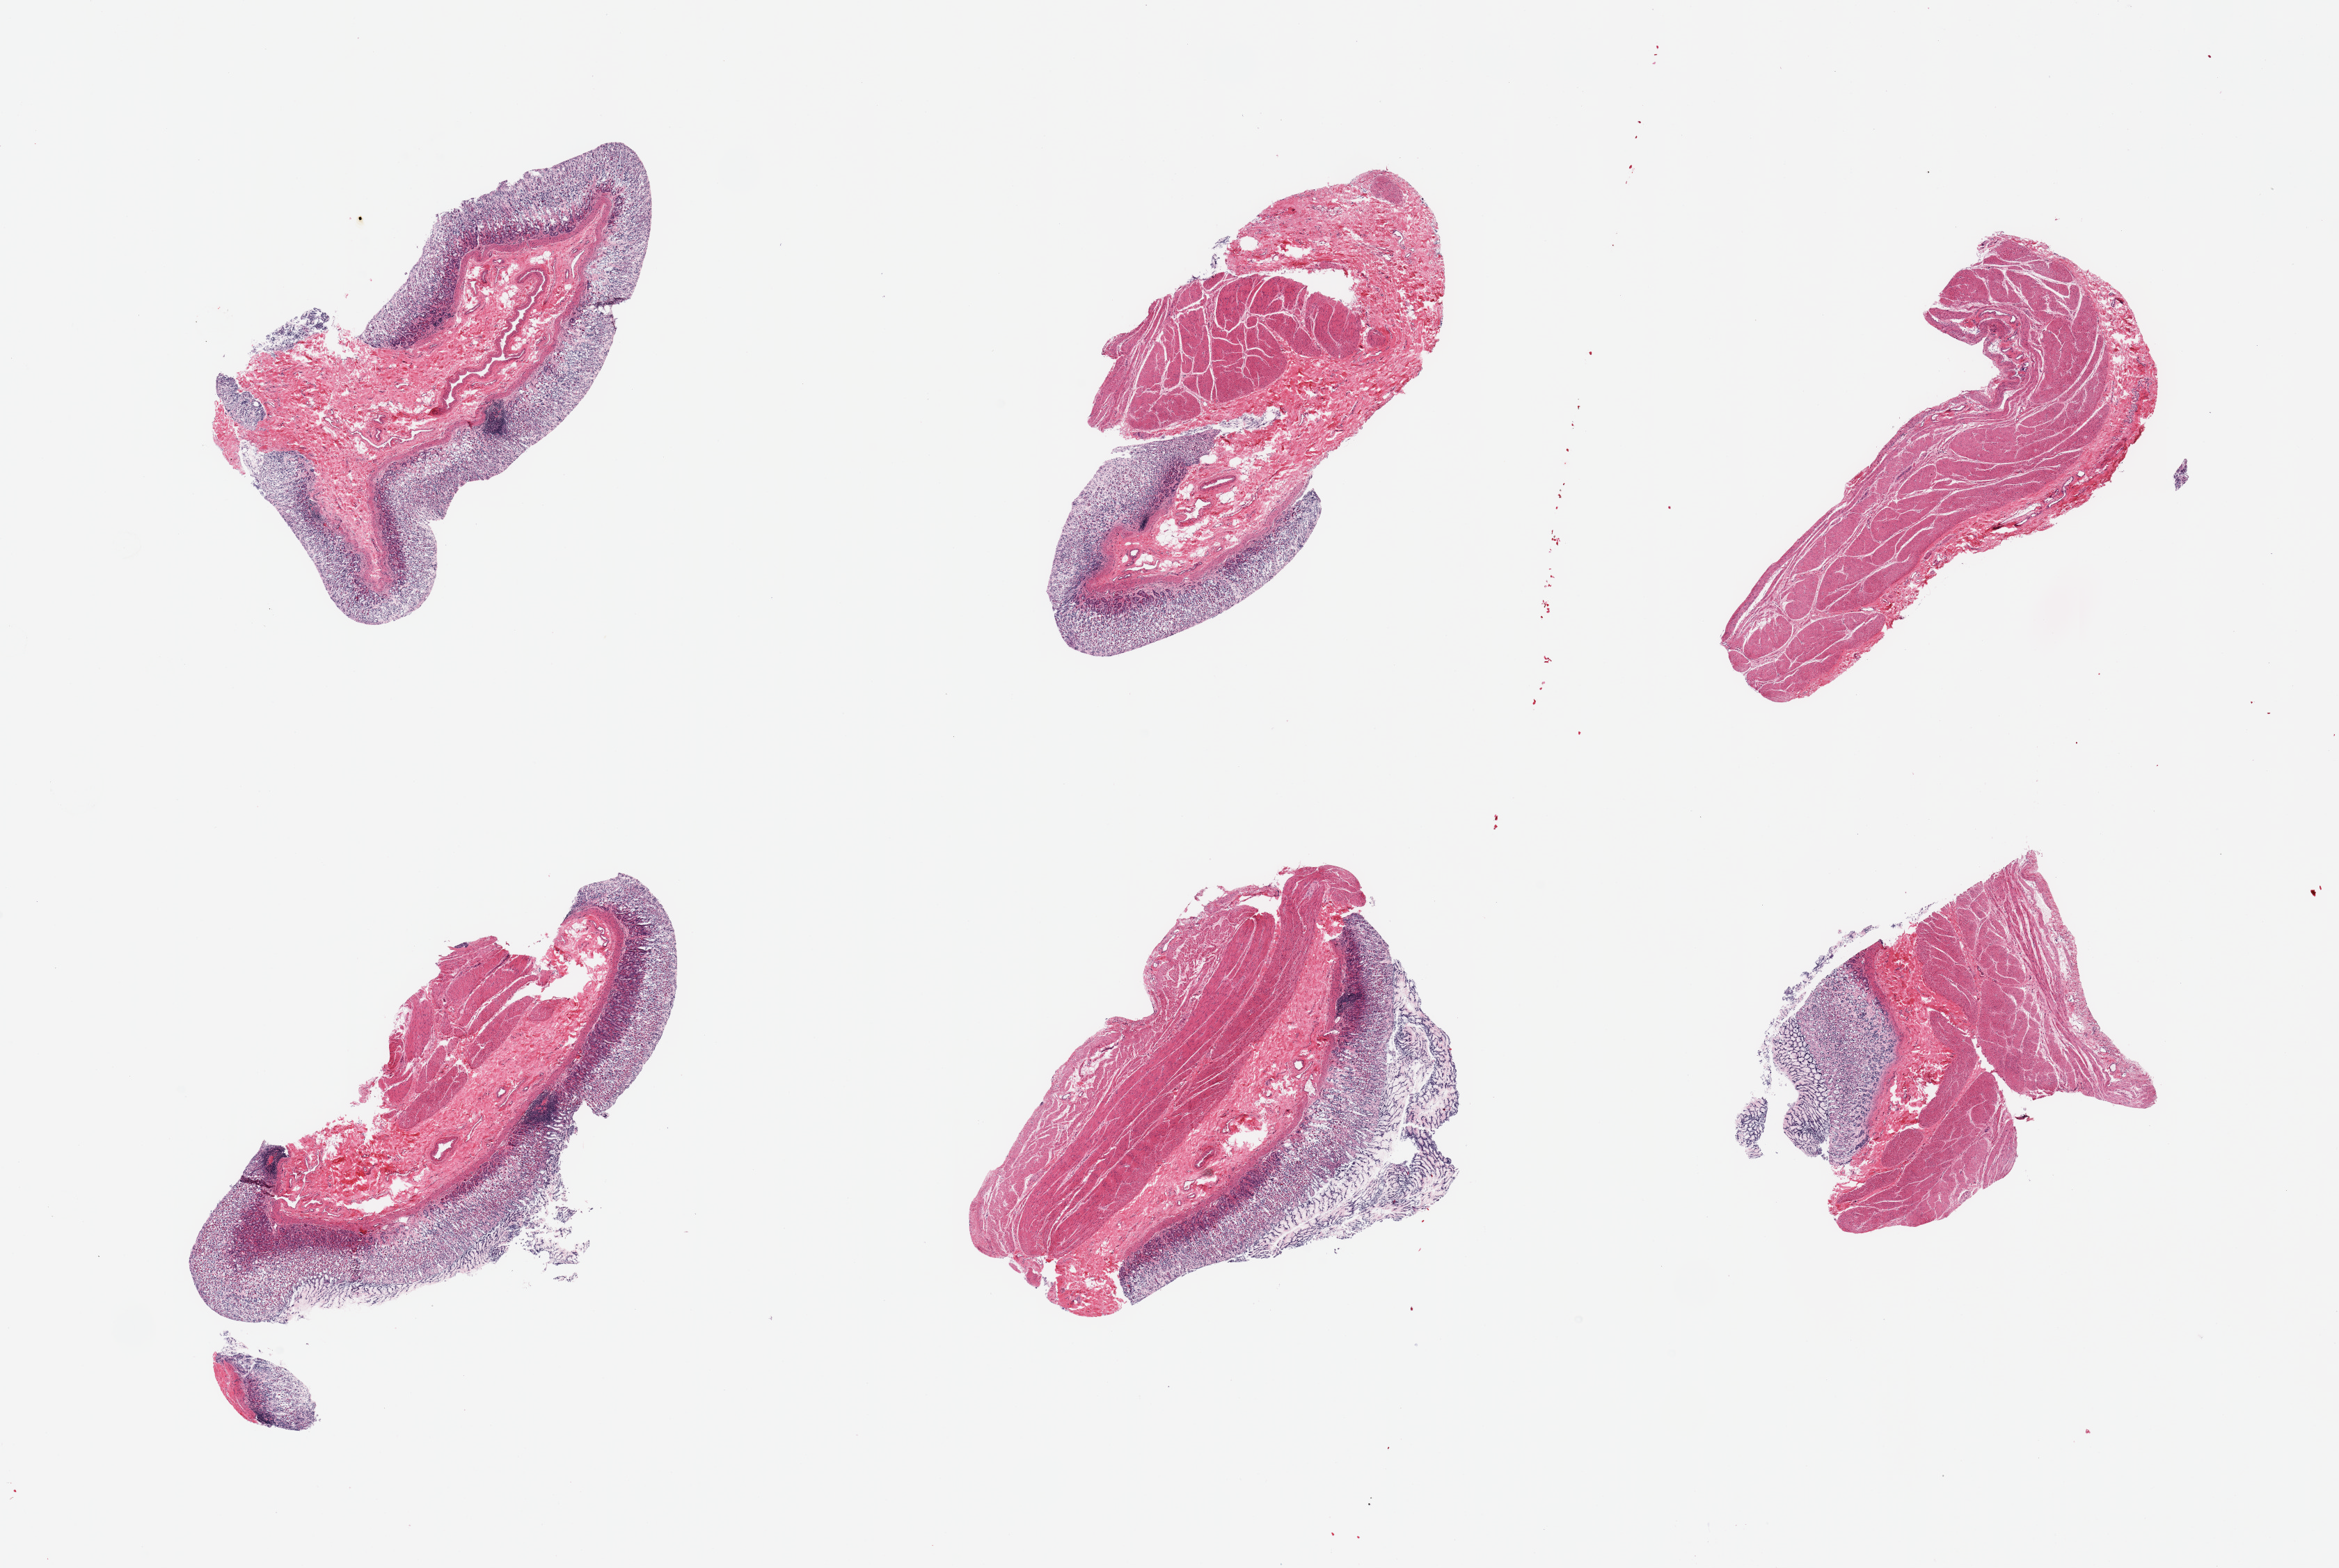
Whole-slide image, hematoxylin and eosin (H&E) stain, whole scanned area (about 26.6 x 17.8 mm) shown as a low-resolution overview. PAXgene-fixed paraffin-embedded (PFPE) section. Section of stomach (target tissue). Tissue donor sample. Female donor.
Reviewer comment on this tissue sample: 6 pieces; mucosa largely autolyzed; muscularis (present in 5 of 6 pieces) moderately autolyzed.